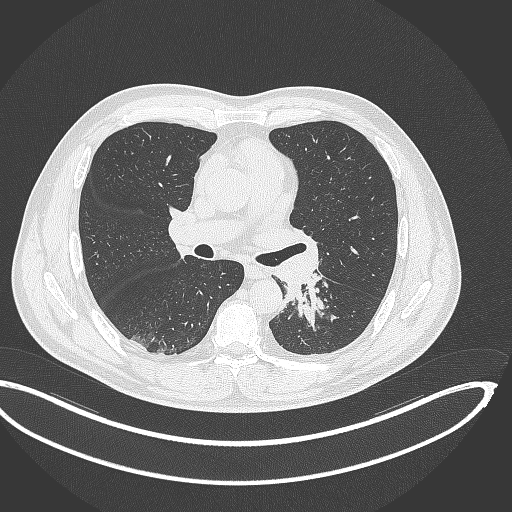
Chest CT, one axial slice; position 202 of 362 along the scan axis; reconstruction kernel B70f; 120 kVp; lung window (W 1500 / L -600 HU); 1 mm slice thickness; 512 × 512 image matrix. Male patient, age 50 years. From the clinical record (not read from this slice): clinical TNM (as recorded): T2a N3 M0.
Annotated regions visible in this slice (bounding box drawn by a radiologist):
- lung tumour (recorded histology: squamous cell carcinoma): bounding box <281,269,327,329> (left, top, right, bottom; pixels)